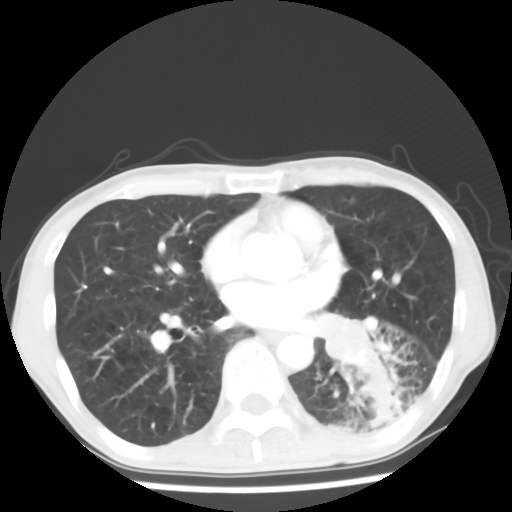
Chest CT, one axial slice; position 29 of 64 along the scan axis; lung window (W 1500 / L -600 HU); 5 mm slice thickness; 512 × 512 image matrix. Patient: male, 68 years. From the clinical record (not read from this slice): clinical TNM (as recorded): T4 N0 M0.
Structures marked on this image (rectangle marked by the reading radiologist):
- lung tumour (recorded histology: squamous cell carcinoma): box from (x=313, y=306) to (x=375, y=373) px